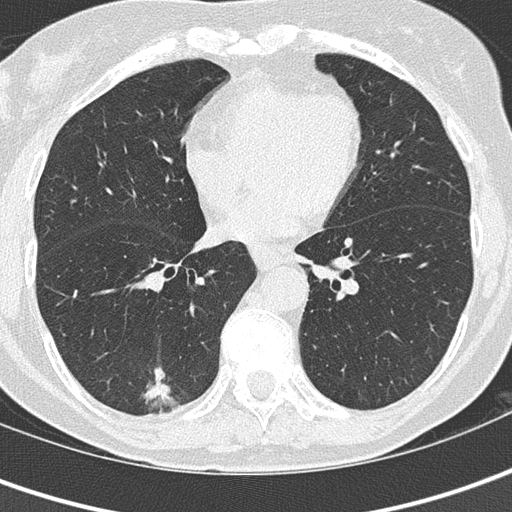
Chest CT (low-dose screening protocol), one axial image. Second annual screen. Lung window (W 1500 / L -600 HU). 2 mm slice thickness. Lung (sharp) reconstruction kernel (B50f). 120 kVp. Slice 90 of 152 in the series. 512 × 512 image matrix, field of view 280 × 280 mm. Female, age 69 years at enrolment. Current smoker at enrolment.
- Expert reader's lesion annotation, bounding box (x1, y1, x2, y2) in pixels: (122, 363, 183, 423).
- The screening reader recorded 2 non-calcified nodules or masses ≥4 mm on this exam (right lower lobe, left lower lobe); which of them this box marks is not recorded.